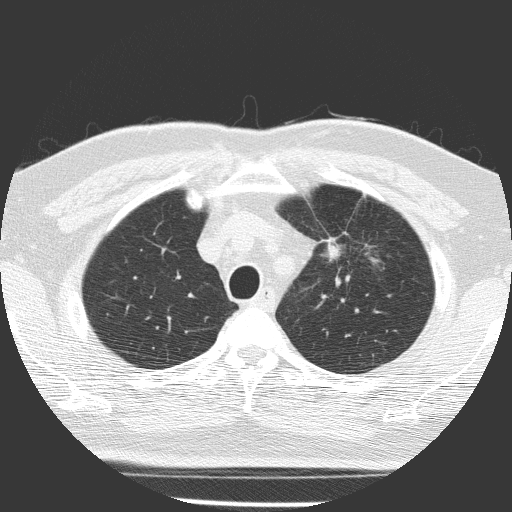
Axial slice from a low-dose chest CT screening exam. First (baseline) screen. Lung window (W 1500 / L -600 HU). 2 mm slice thickness. Lung (sharp) reconstruction kernel (FC51). Male, age 70 years at enrolment.
- Lesion marked by an expert reader, bounding box <296,217,373,291> (left, top, right, bottom; pixels).
- The screening reader recorded 3 non-calcified nodules or masses ≥4 mm on this exam (left upper lobe, left lower lobe, left upper lobe); which of them this box marks is not recorded.
- Lung cancer was diagnosed 58 days after this screen: squamous cell carcinoma, NOS, left upper lobe, poorly differentiated (G3), stage IB (AJCC 6th edition), 47 mm at pathology.